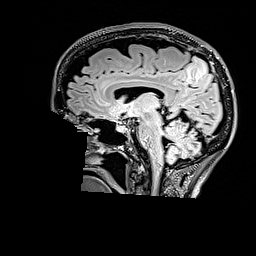
Brain MRI from a brain-tumour surgery series, one sagittal slice. T2 FLAIR. 1 mm slice thickness. 256 × 256 image matrix, field of view 256 × 256 mm. From the clinical record (not read from this slice): histopathology: Astrocytoma; WHO grade: 3; IDH mutation: yes; tumour location: Right Parietal.
Structures marked on this image (expert manual segmentation):
- tumour: bounding box <184,56,212,82> (left, top, right, bottom; pixels)
- tumour: <184,57,208,82>